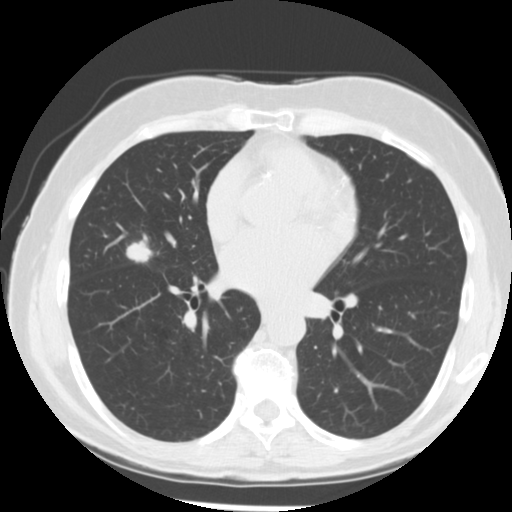
Low-dose screening chest CT, one axial slice. Position 133 of 255 along the scan axis. Reconstruction kernel STANDARD. Lung window (W 1500 / L -600 HU). 512 × 512 image matrix, field of view 320 × 320 mm.
Annotated regions visible in this slice (expert manual segmentation):
- lesion 1 (tumor, middle lobe of right lung): bounding box <126,240,153,263> (left, top, right, bottom; pixels)